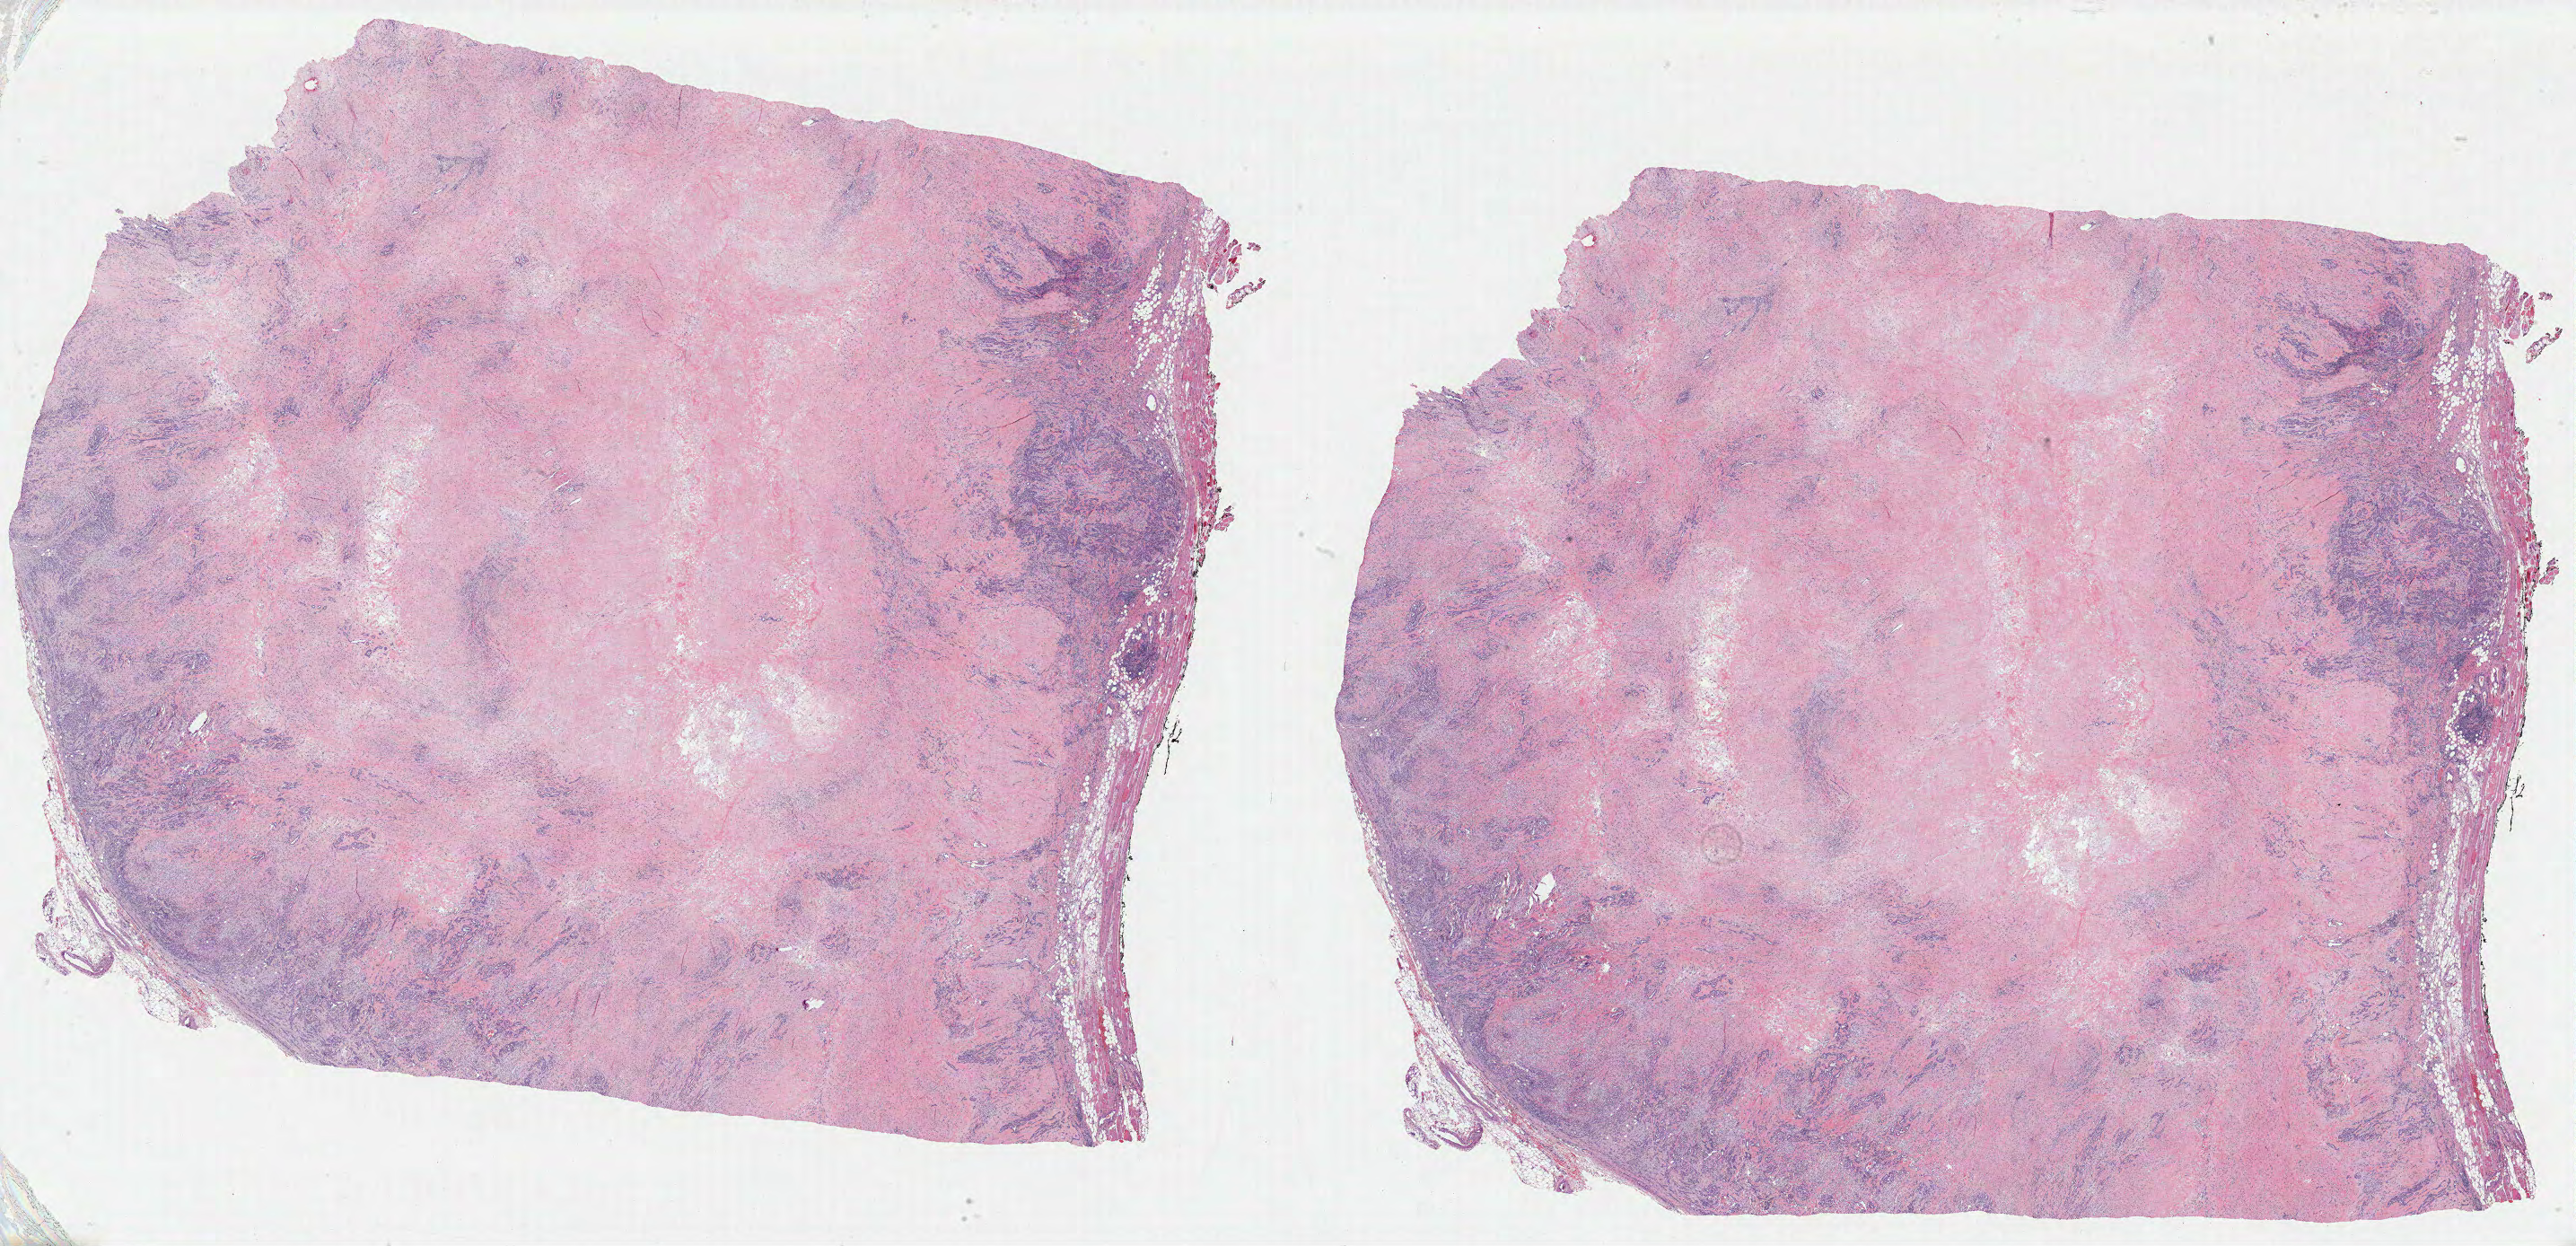
H&E whole-slide image, shown as a low-resolution overview of the whole scanned area (about 45.8 x 22.2 mm), formalin-fixed paraffin-embedded (FFPE) diagnostic section, primary tumour sample from the mesothelium. Patient: male, age at initial diagnosis 80 years.
Pathologic diagnosis: Mesothelioma, biphasic, malignant (pleura, NOS).